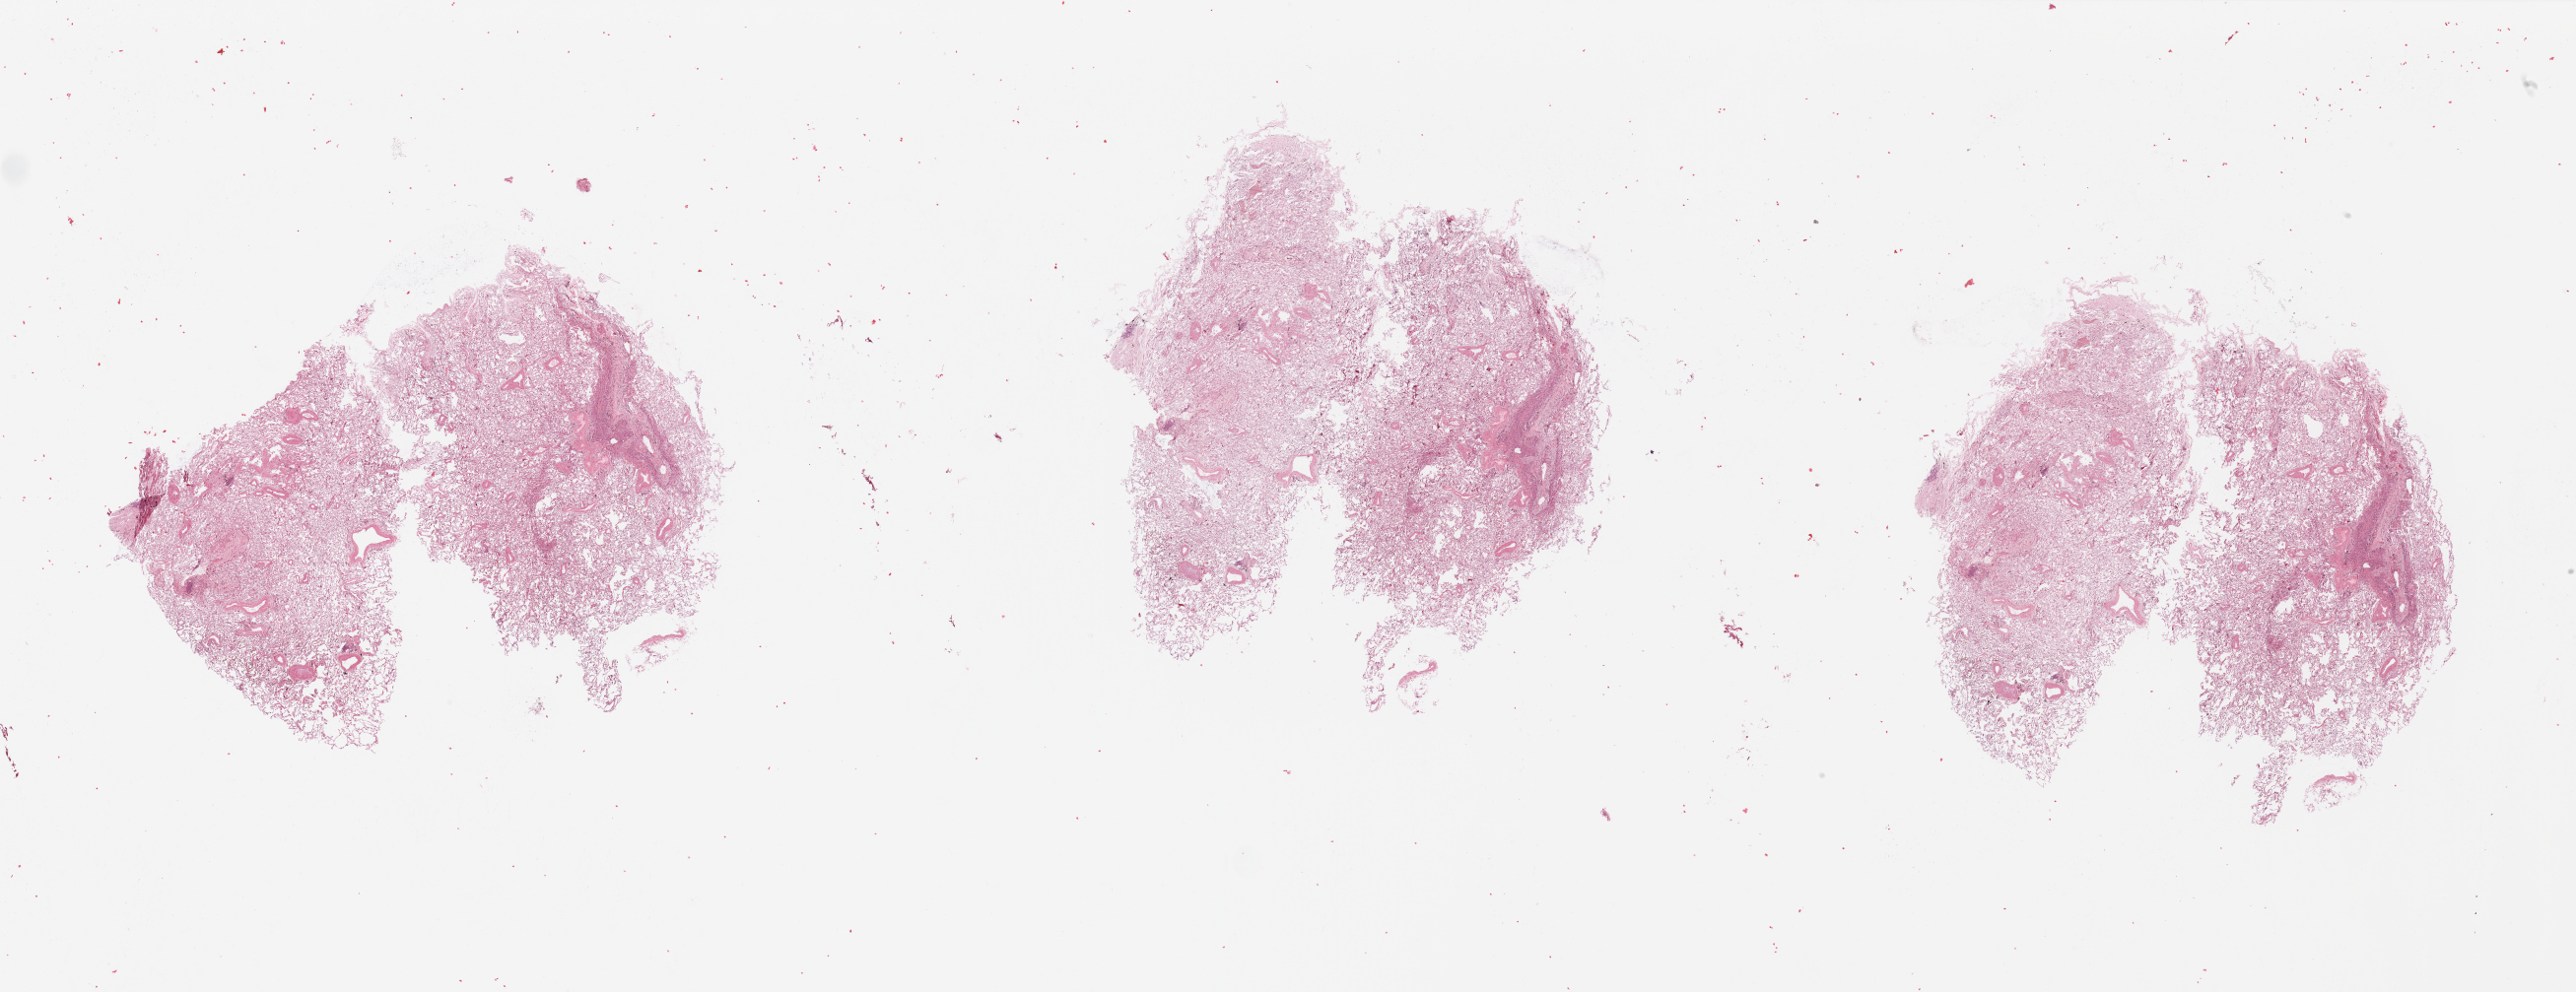
H&E-stained whole-slide image — low-resolution overview of the scanned area, about 41.3 x 15.9 mm (slide scanned at 20x). Lung, tissue type not recorded.
Patient diagnosis (cohort enrolment): lung adenocarcinoma (lung).